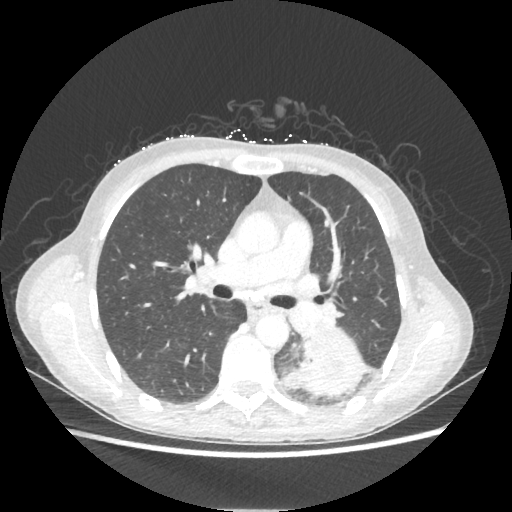
Chest CT, one axial slice. Slice 130 of 221 in the series (ordered by position). 80 kVp. Lung window (W 1500 / L -600 HU). 1.25 mm slice thickness. 512 × 512 image matrix, field of view 360 × 360 mm. Patient: female, 53 years. Case-level facts recorded for this patient, not image findings: clinical TNM (as recorded): T3 N0 M0.
Outlined on this slice (bounding box drawn by a radiologist):
- lung tumour (recorded histology: adenocarcinoma): box from (x=282, y=330) to (x=370, y=396) px